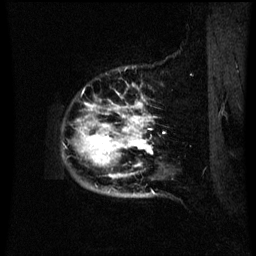
Breast MRI (dynamic contrast-enhanced), one sagittal slice; slice 59 of 60 in the series (ordered by position); dynamic contrast-enhanced series, image 2 of 3 at this slice position (ordered by acquisition); 1.5 T; TE 4.2 ms, TR 8.9 ms; 2.1 mm slice thickness; 256 × 256 image matrix, field of view 200 × 200 mm. Female patient, age 42 years. Case-level facts recorded for this patient, not image findings: setting: breast cancer imaged before/during neoadjuvant chemotherapy; receptor status: HER2-positive.
Outlined on this slice (semi-automatic segmentation, software-assisted and operator-edited):
- analysis volume of interest (the breast-tissue region the enhancement analysis was run in; not a lesion): bounding box (x1, y1, x2, y2) in pixels: (66, 90, 169, 193)
- tumour enhancement mask (voxels above the 70 % enhancement threshold inside the analysis volume of interest): (80, 102, 153, 177)